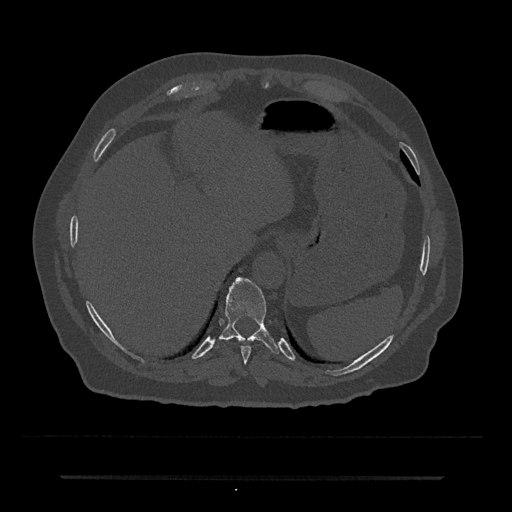
CT including the spine, one axial slice. Reconstruction kernel Br40s/3. Bone window (W 1800 / L 400 HU). 0.5 mm slice thickness. 512 × 512 image matrix, field of view 437 × 437 mm. Patient: male, 69 years. Case-level facts recorded for this patient, not image findings: primary cancer: prostate.
Annotated regions visible in this slice (semi-automatic segmentation, software-assisted and operator-edited):
- T10 vertebra: bounding box (x1, y1, x2, y2) in pixels: (220, 277, 279, 354)
- T9 vertebra: (241, 346, 251, 364)